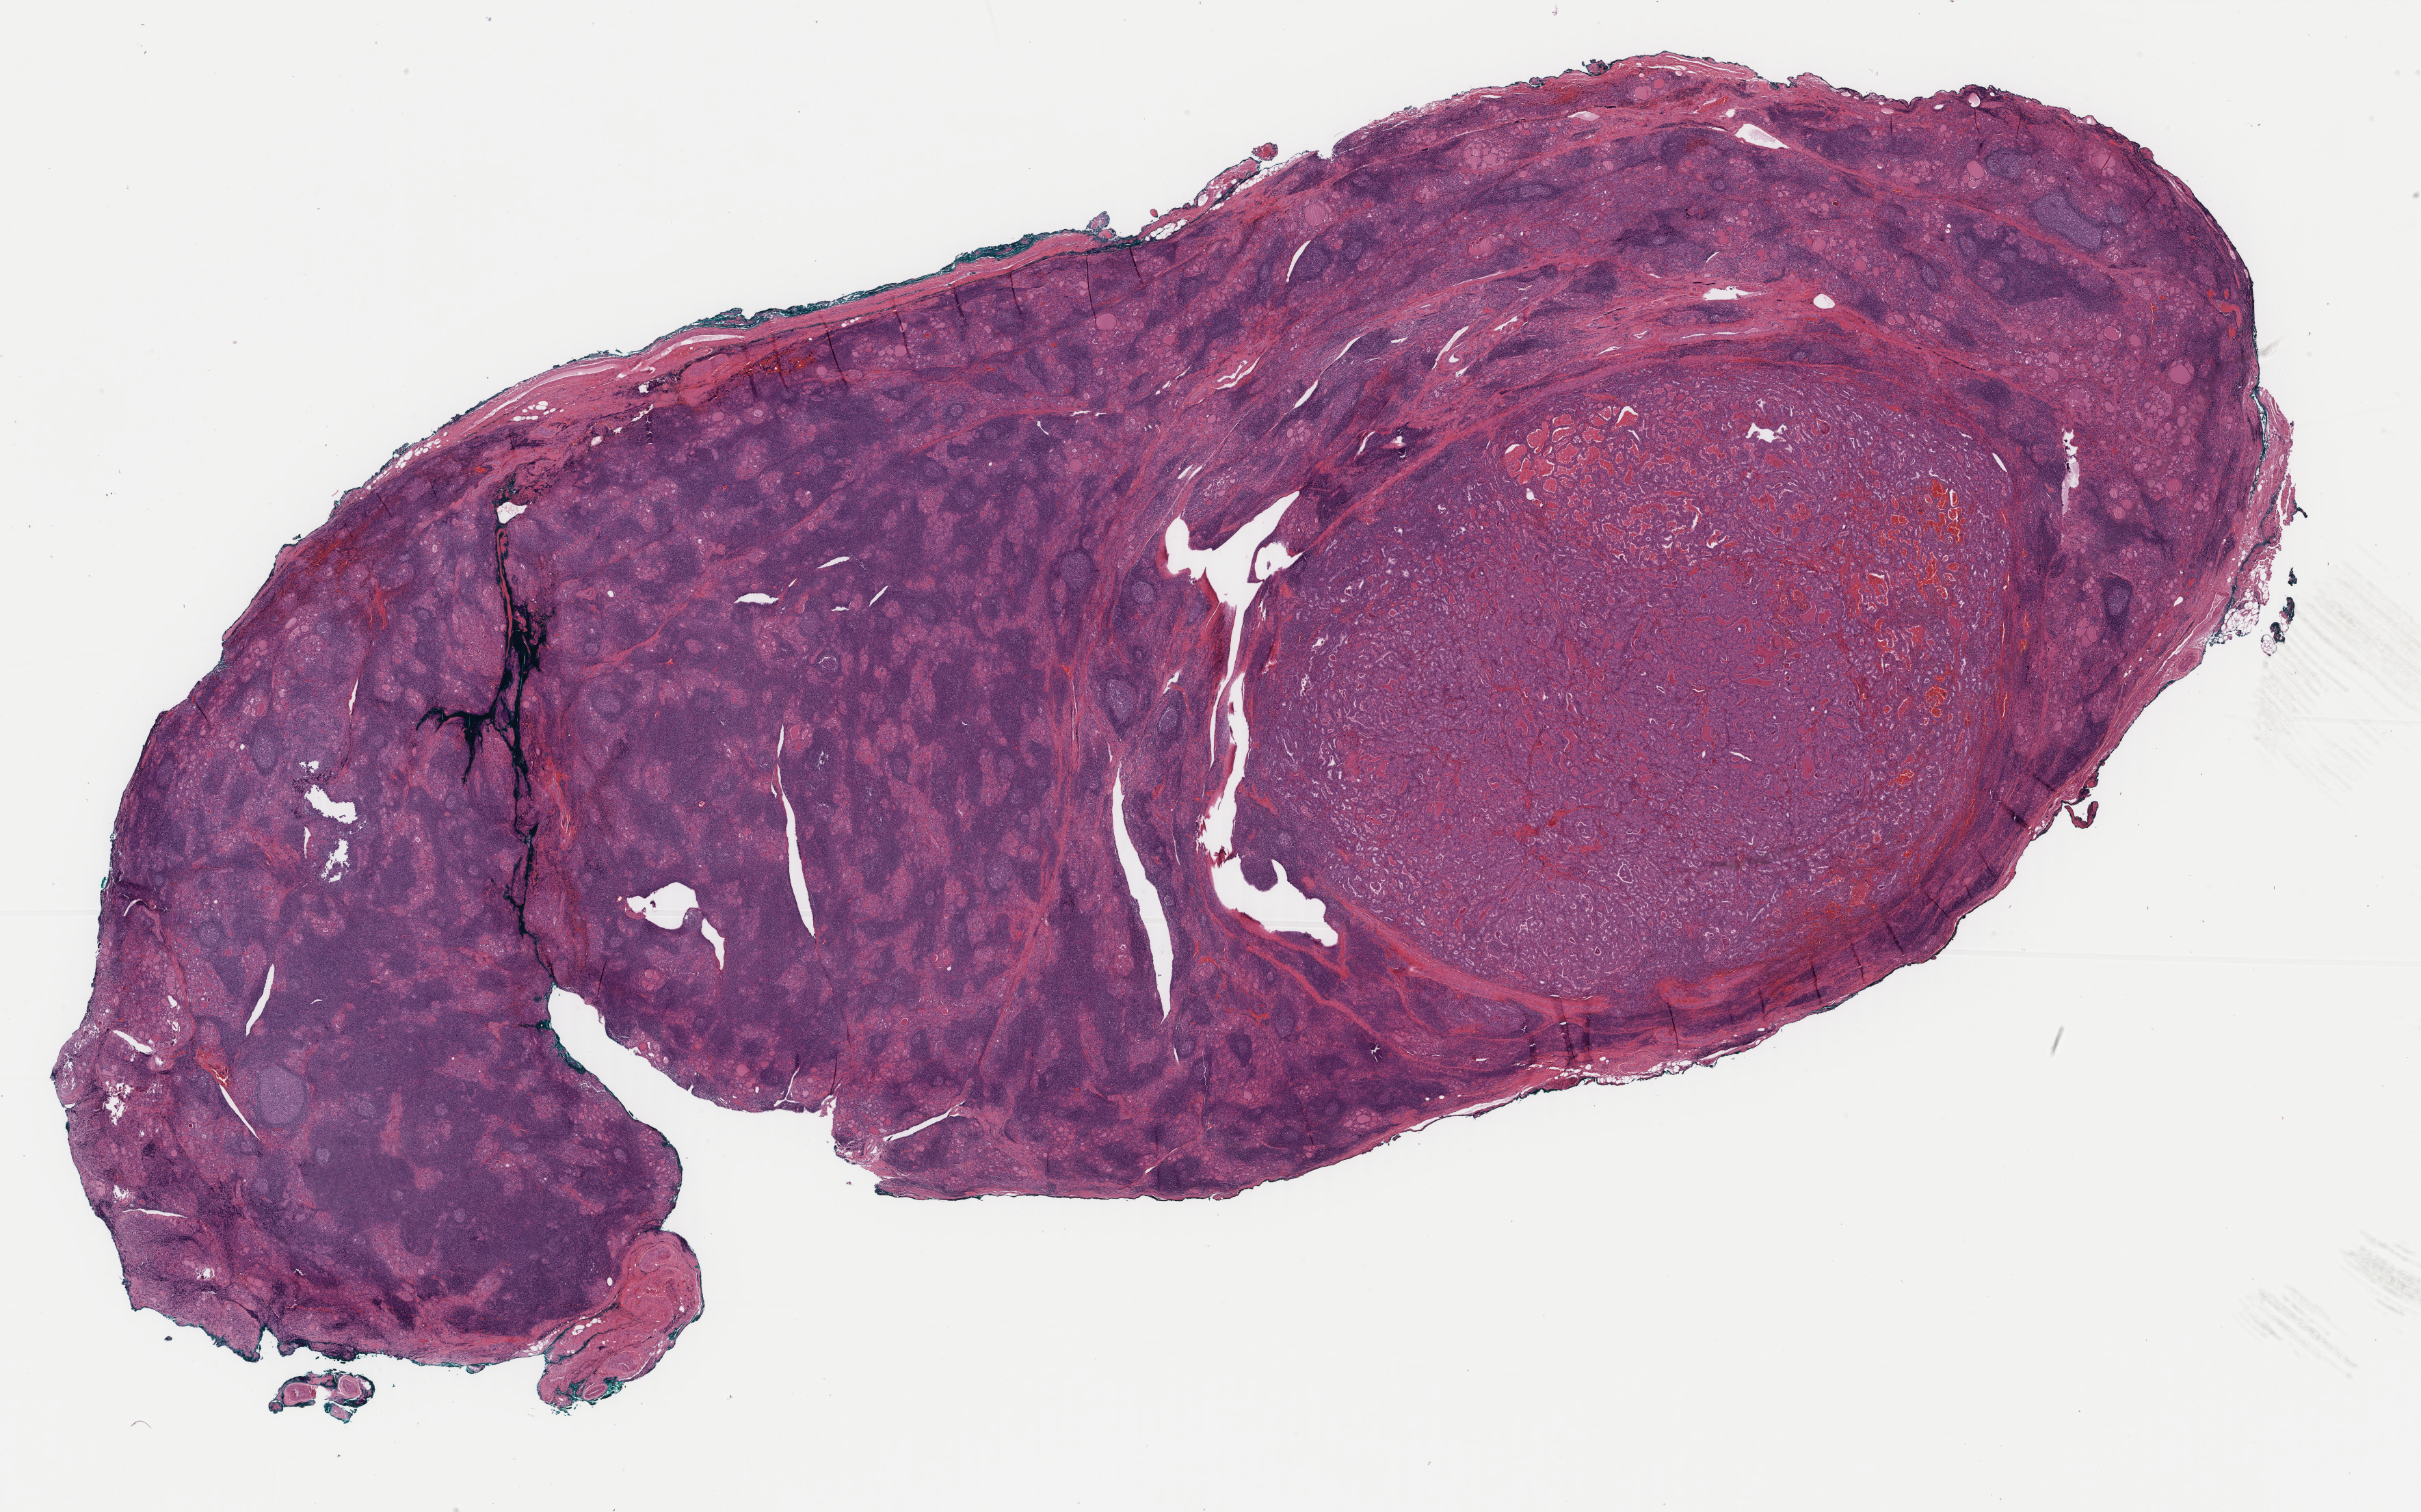
H&E whole-slide image — shown as a low-resolution overview of the whole scanned area (about 28.1 x 17.5 mm), FFPE section, sample: primary tumour, thyroid. Female, age 55 years at initial diagnosis.
Laterality: right. Histologic diagnosis: Papillary carcinoma, follicular variant (thyroid gland). Lymph nodes positive (case pathology): 0 of 13 examined. AJCC pathologic stage: I. TNM: T1 N0 M0.